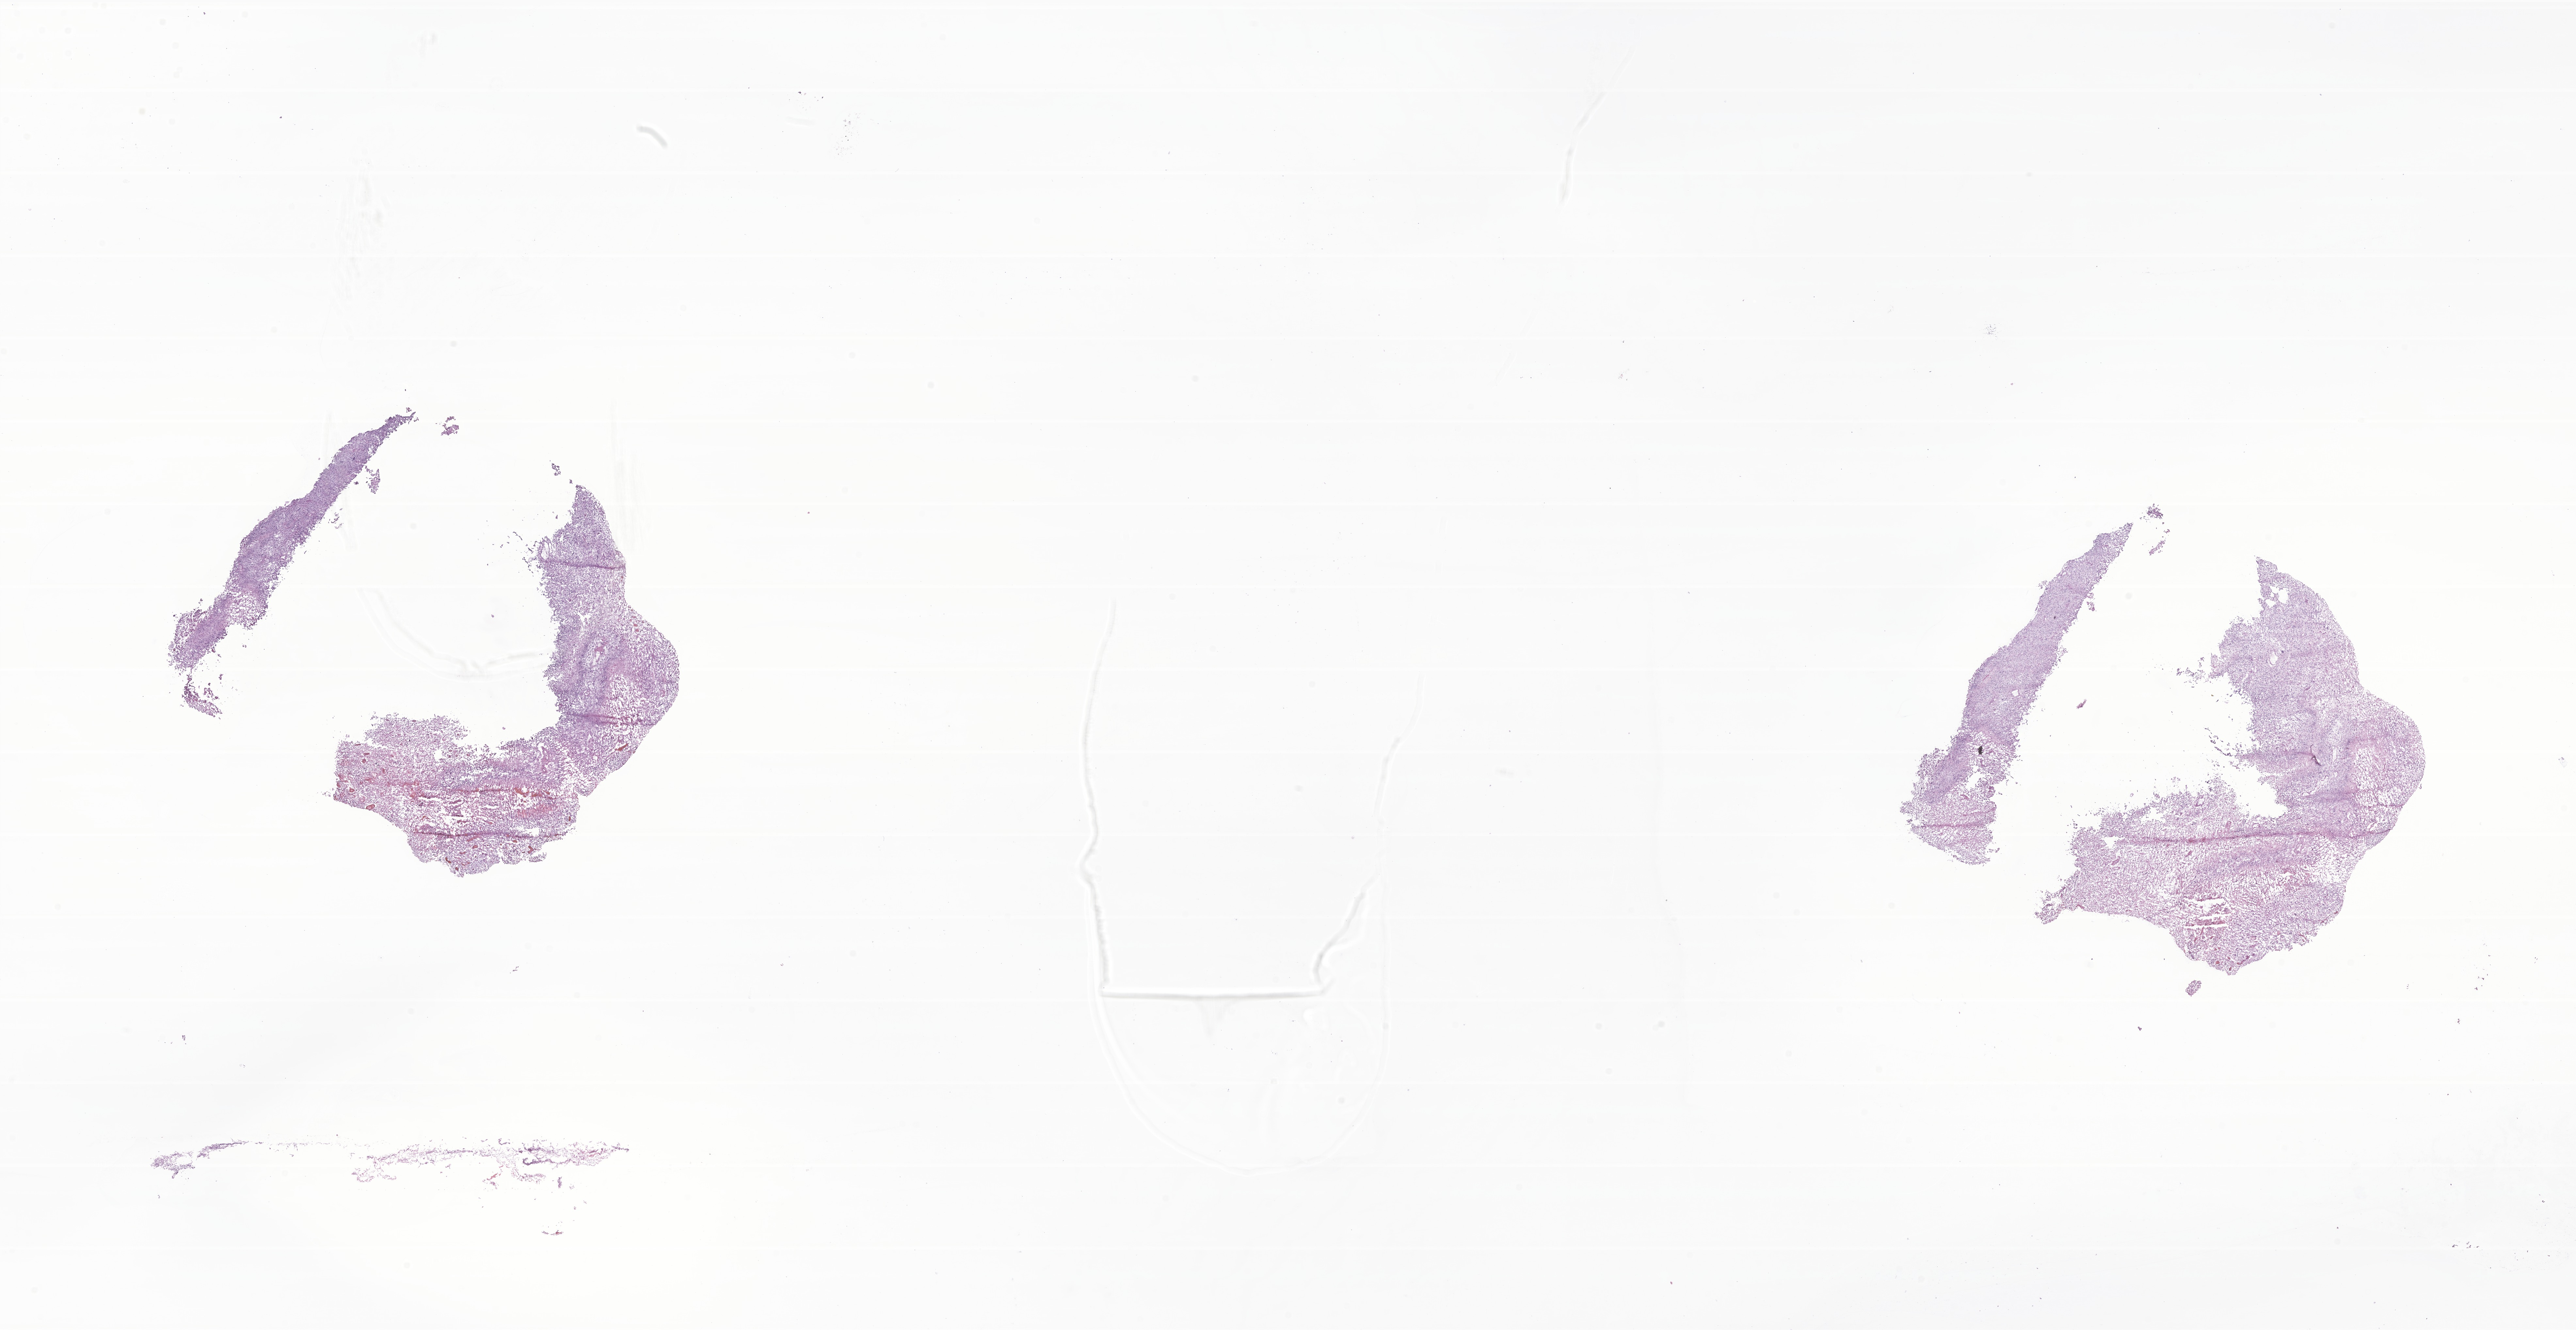
Digitized H&E-stained section of tumor tissue from the brain, low-resolution overview of the scanned area, about 33.3 x 17.2 mm, frozen section. Female patient, age 154 months (12 years 10 months).
* diagnosis: Glioma, malignant